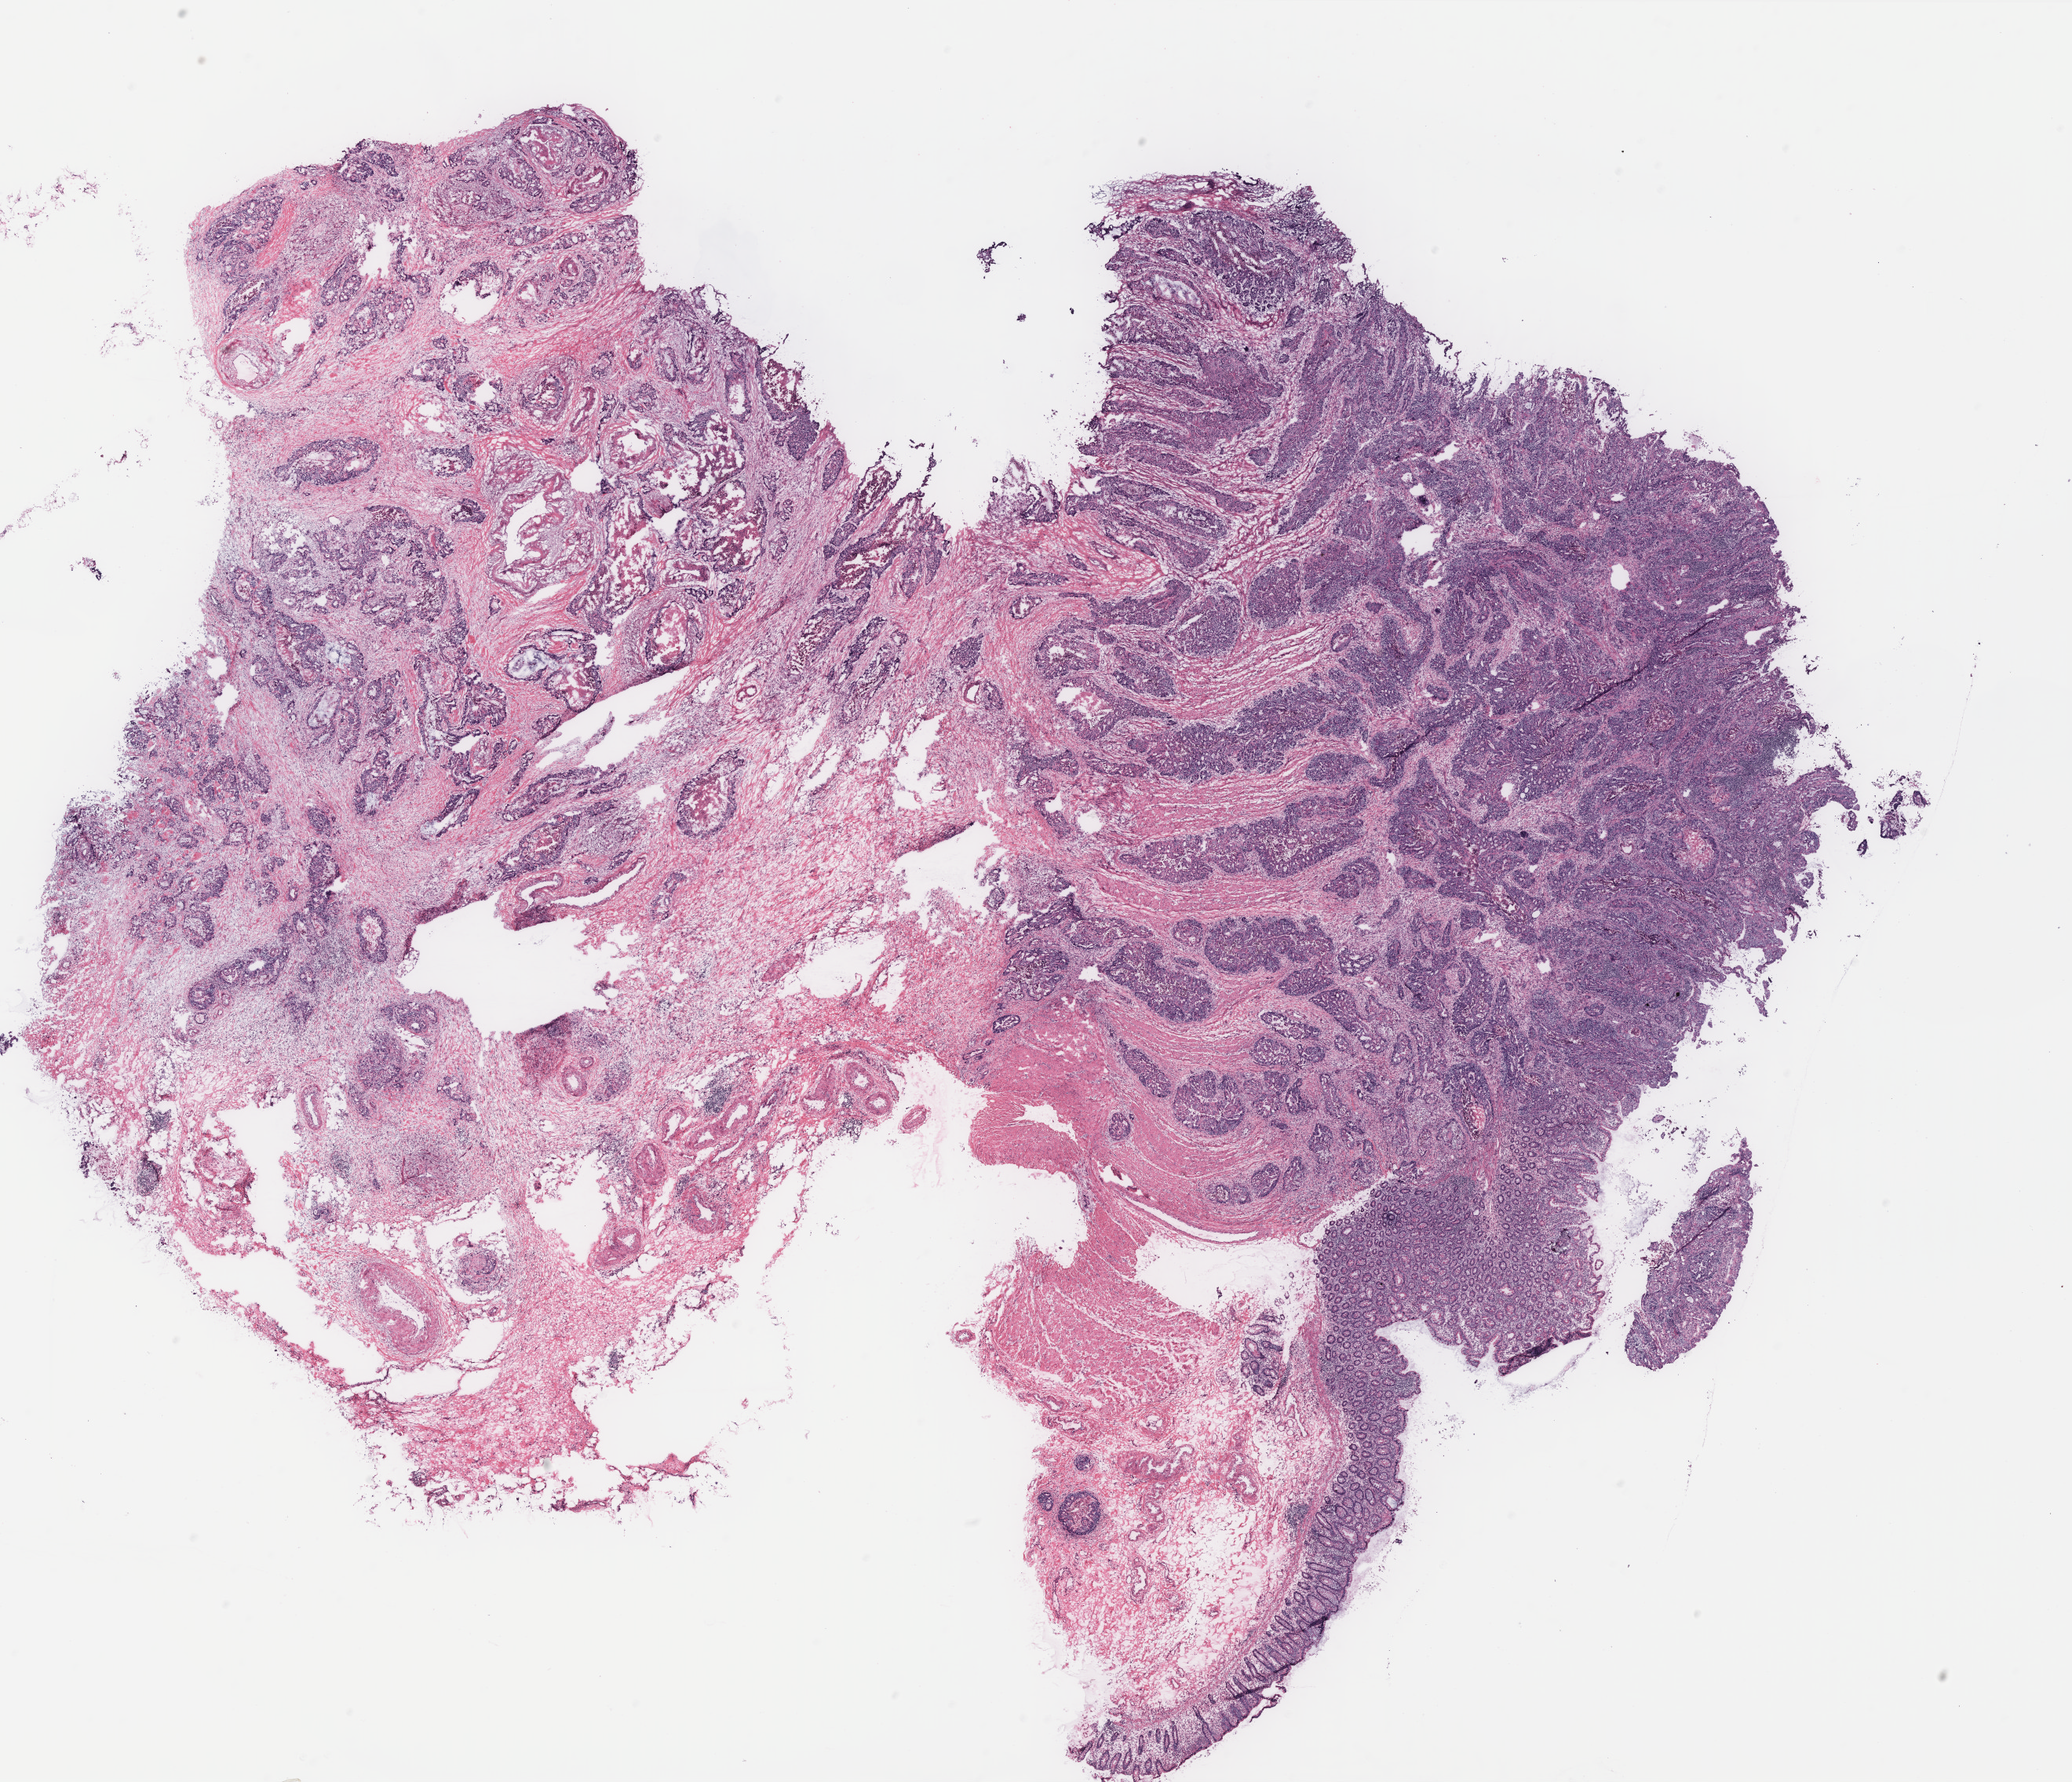
Whole-slide histology image, H&E, a low-resolution overview of the entire scanned area, about 21.1 x 18.2 mm. Colon, tissue type not recorded.
Patient diagnosis (cohort enrolment): colon cancer (colon).